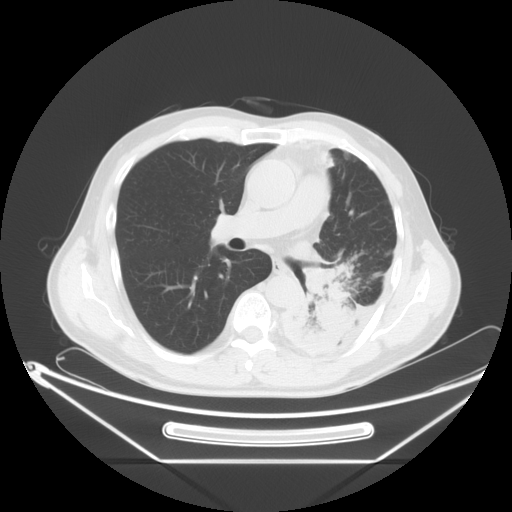
Chest CT, one axial slice. Position 36 of 63 along the scan axis. Reconstruction kernel STANDARD. 120 kVp. Lung window (W 1500 / L -600 HU). 512 × 512 image matrix. Male patient, age 60 years. Case-level facts recorded for this patient, not image findings: clinical TNM (as recorded): T4 N1 M1.
Outlined on this slice (rectangle marked by the reading radiologist):
- lung tumour (recorded histology: adenocarcinoma): bounding box (x1, y1, x2, y2) in pixels: (297, 256, 357, 349)